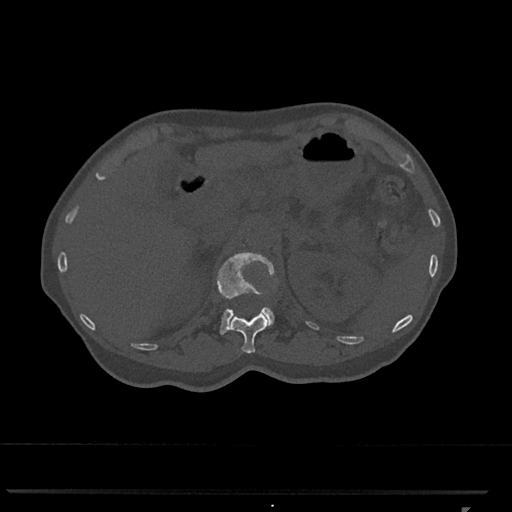
CT including the spine, one axial slice. Slice 435 of 793 in the series (ordered by position). 120 kVp. Bone window (W 1800 / L 400 HU). 512 × 512 image matrix. Patient: female, 62 years. From the clinical record (not read from this slice): primary cancer: renal.
Structures marked on this image (semi-automatically segmented with operator editing):
- L1 vertebra: box from (x=217, y=252) to (x=275, y=335) px
- T12 vertebra: (x=229, y=313)–(x=269, y=354)